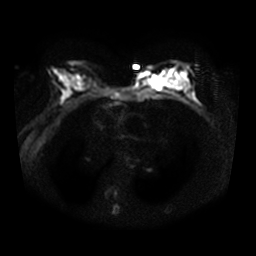
Breast MRI, one axial slice; slice 17 of 32 in the series (ordered by position); diffusion-weighted series; image 2 of 4 stored at this slice position (different b-values; order by instance number); 3 T; 5 mm slice thickness; 256 × 256 image matrix. Female patient.
Annotated regions visible in this slice (manually delineated by an expert):
- tumour on diffusion-weighted imaging: box from (x=149, y=76) to (x=175, y=87) px